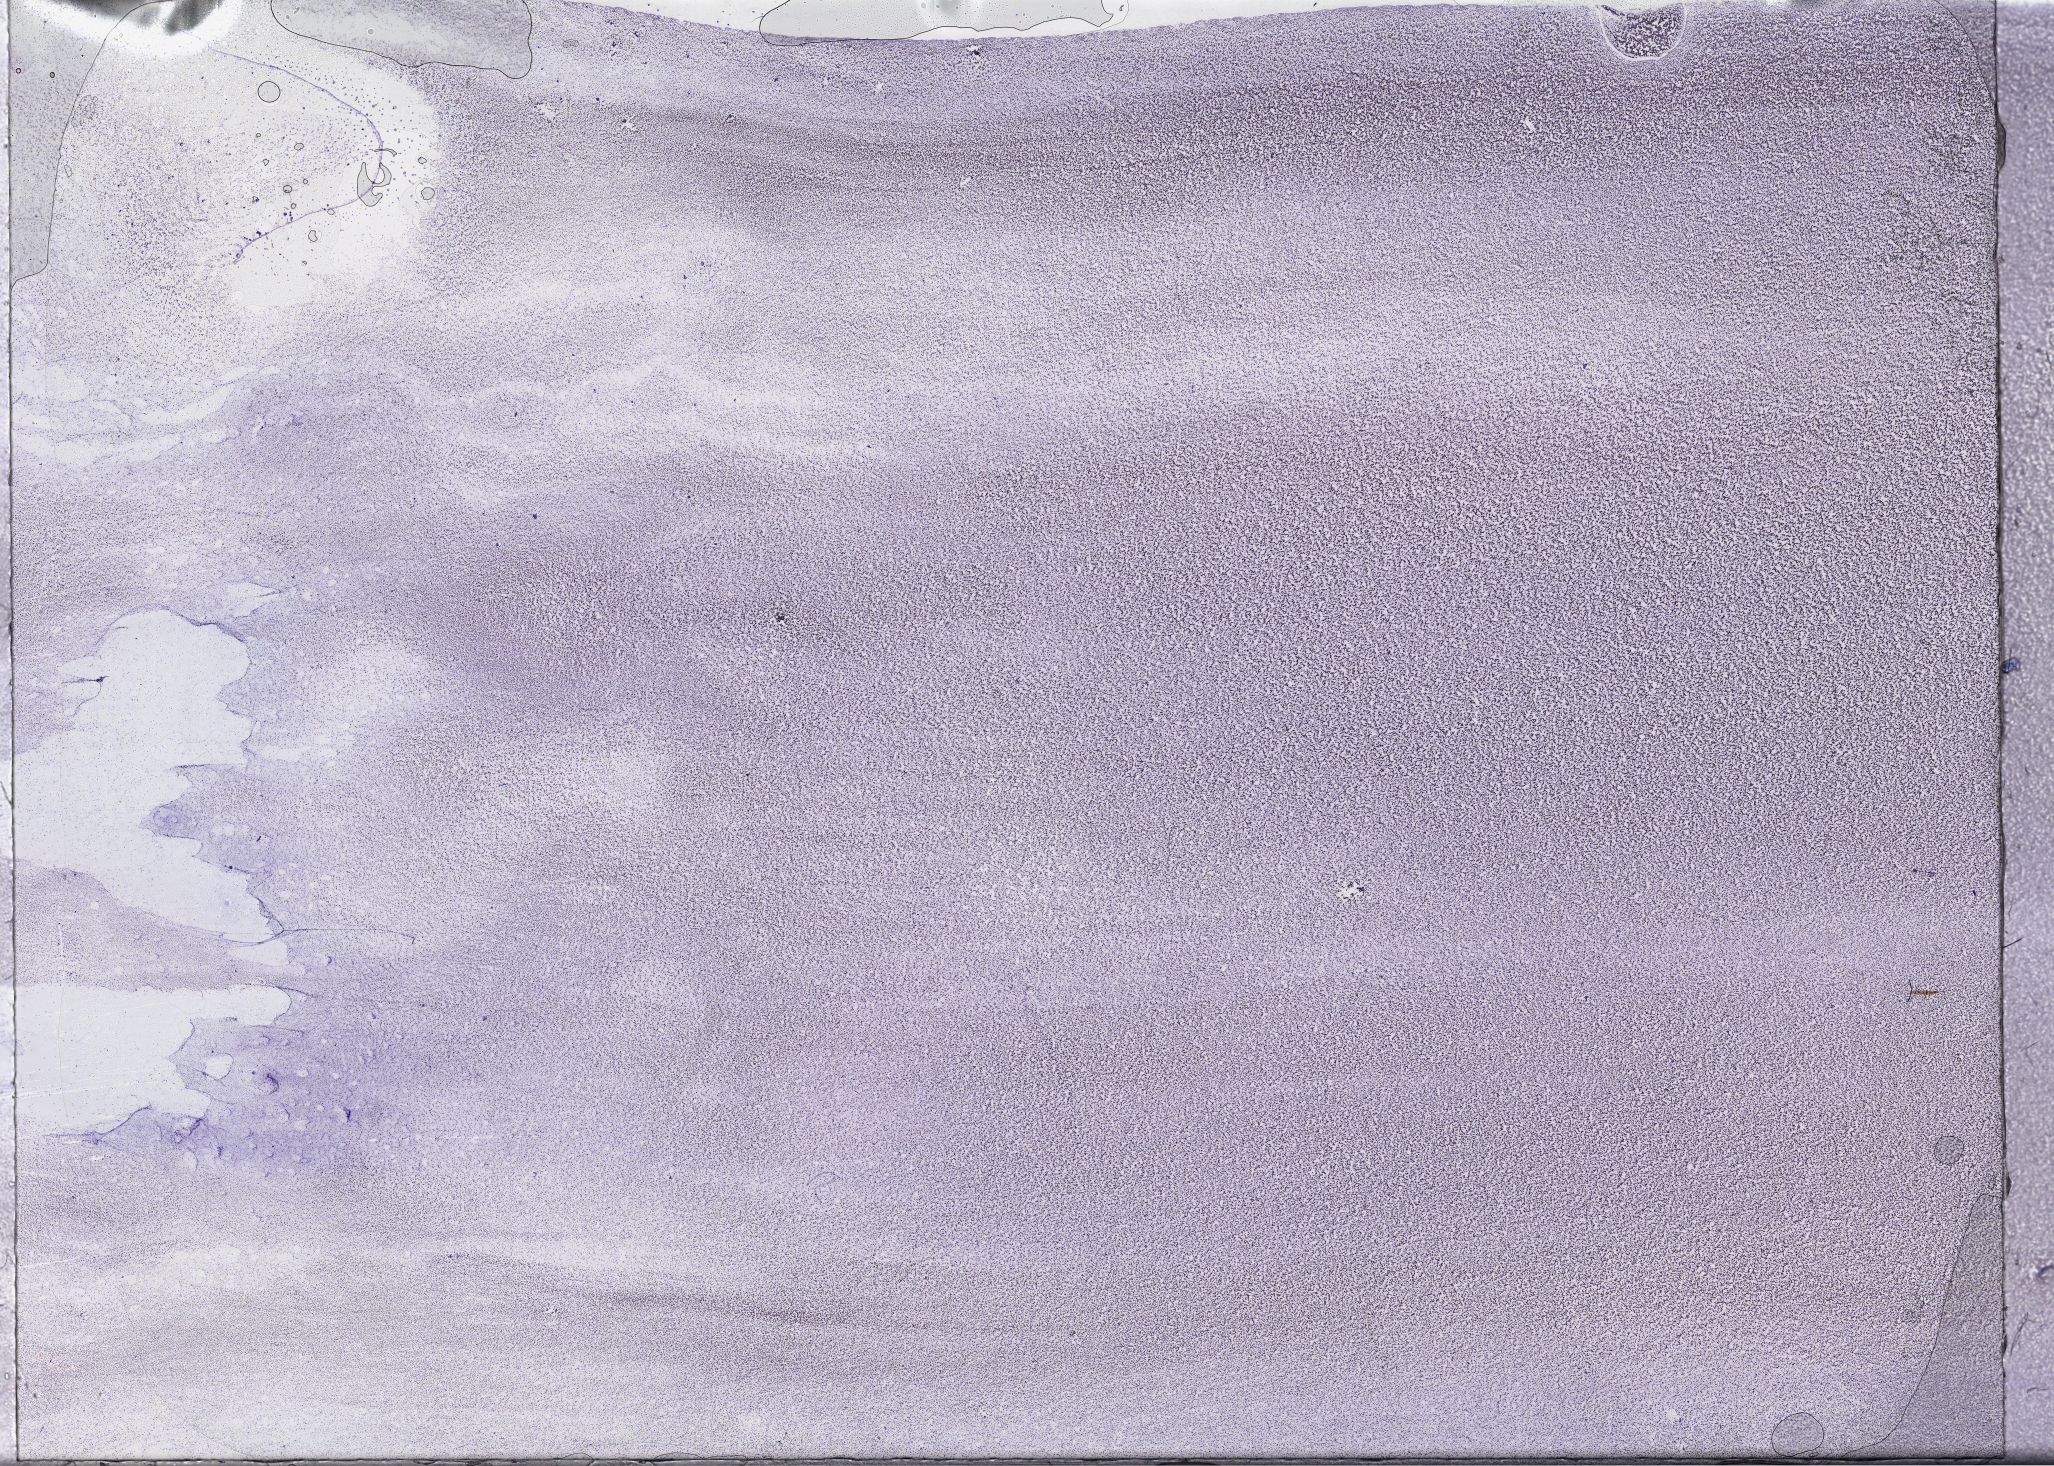
Whole-slide histology image, H&E-stained, whole scanned area (about 33.2 x 23.7 mm, acquisition: 40x scan) shown as a low-resolution overview. Peripheral blood (leukaemic) sample. Patient: female, age 61 years.
Diagnosis: Acute Myeloid Leukemia. WHO classification: Acute myelomonocytic leukemia. FAB classification: M4.